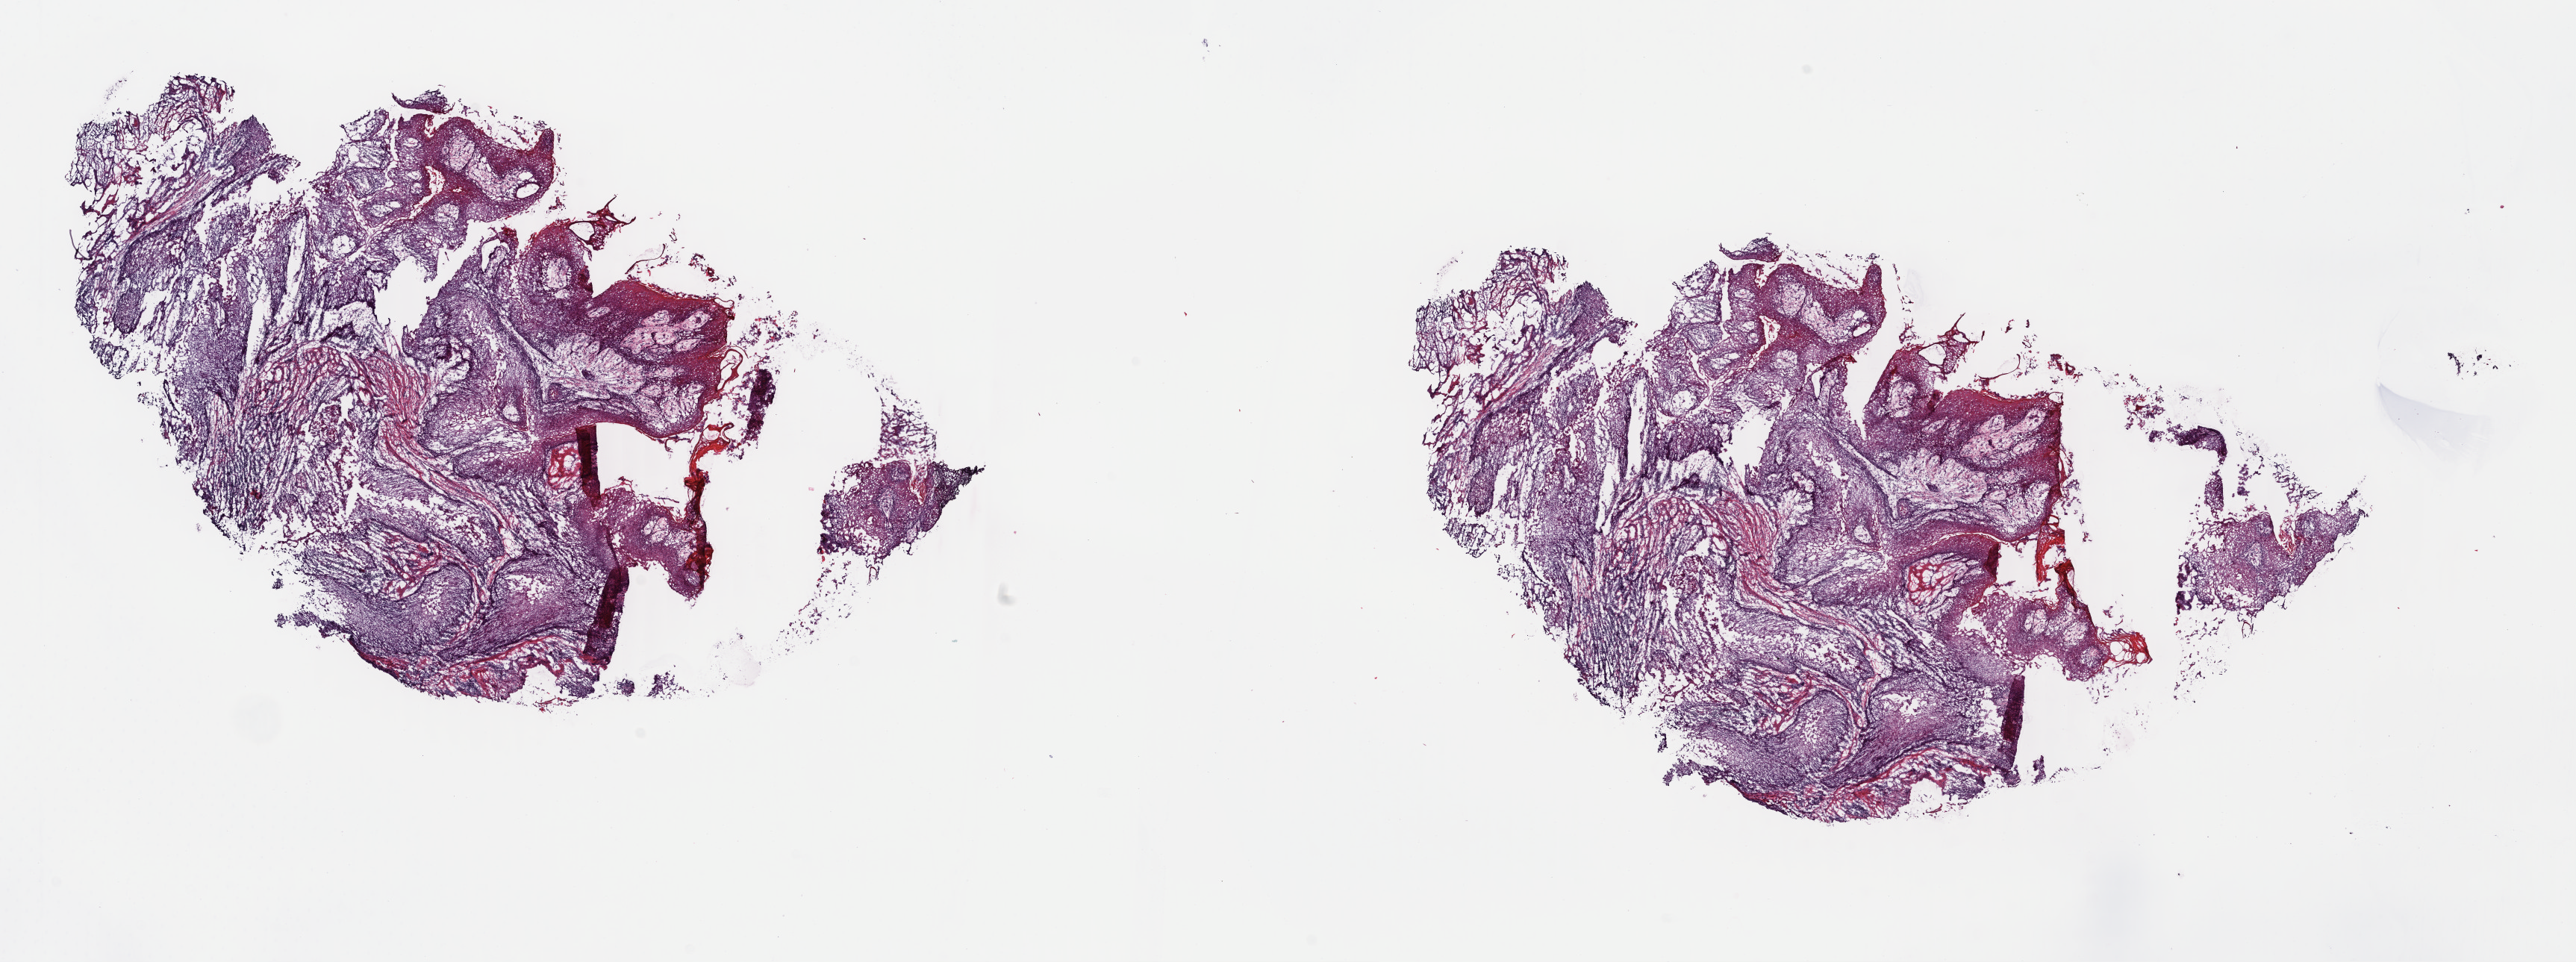
H&E whole-slide image, a low-resolution overview of the entire scanned area, about 27.1 x 10.1 mm (from a 40x scan); frozen section; sample: primary tumour, head and neck. Female, age 87 years at initial diagnosis. Histologic grade: G1 (well differentiated). Pathologist review of this section (percent, as recorded): tumour cells 75%, tumour nuclei 75%, normal cells 15%, stromal cells 5%, necrosis 5%. Inflammatory infiltration, as recorded: lymphocyte infiltration 0%, monocyte infiltration 0%, neutrophil infiltration 0%.
AJCC pathologic stage: IVA (5th edition). Pathologic diagnosis: Squamous cell carcinoma, NOS (mouth, NOS).